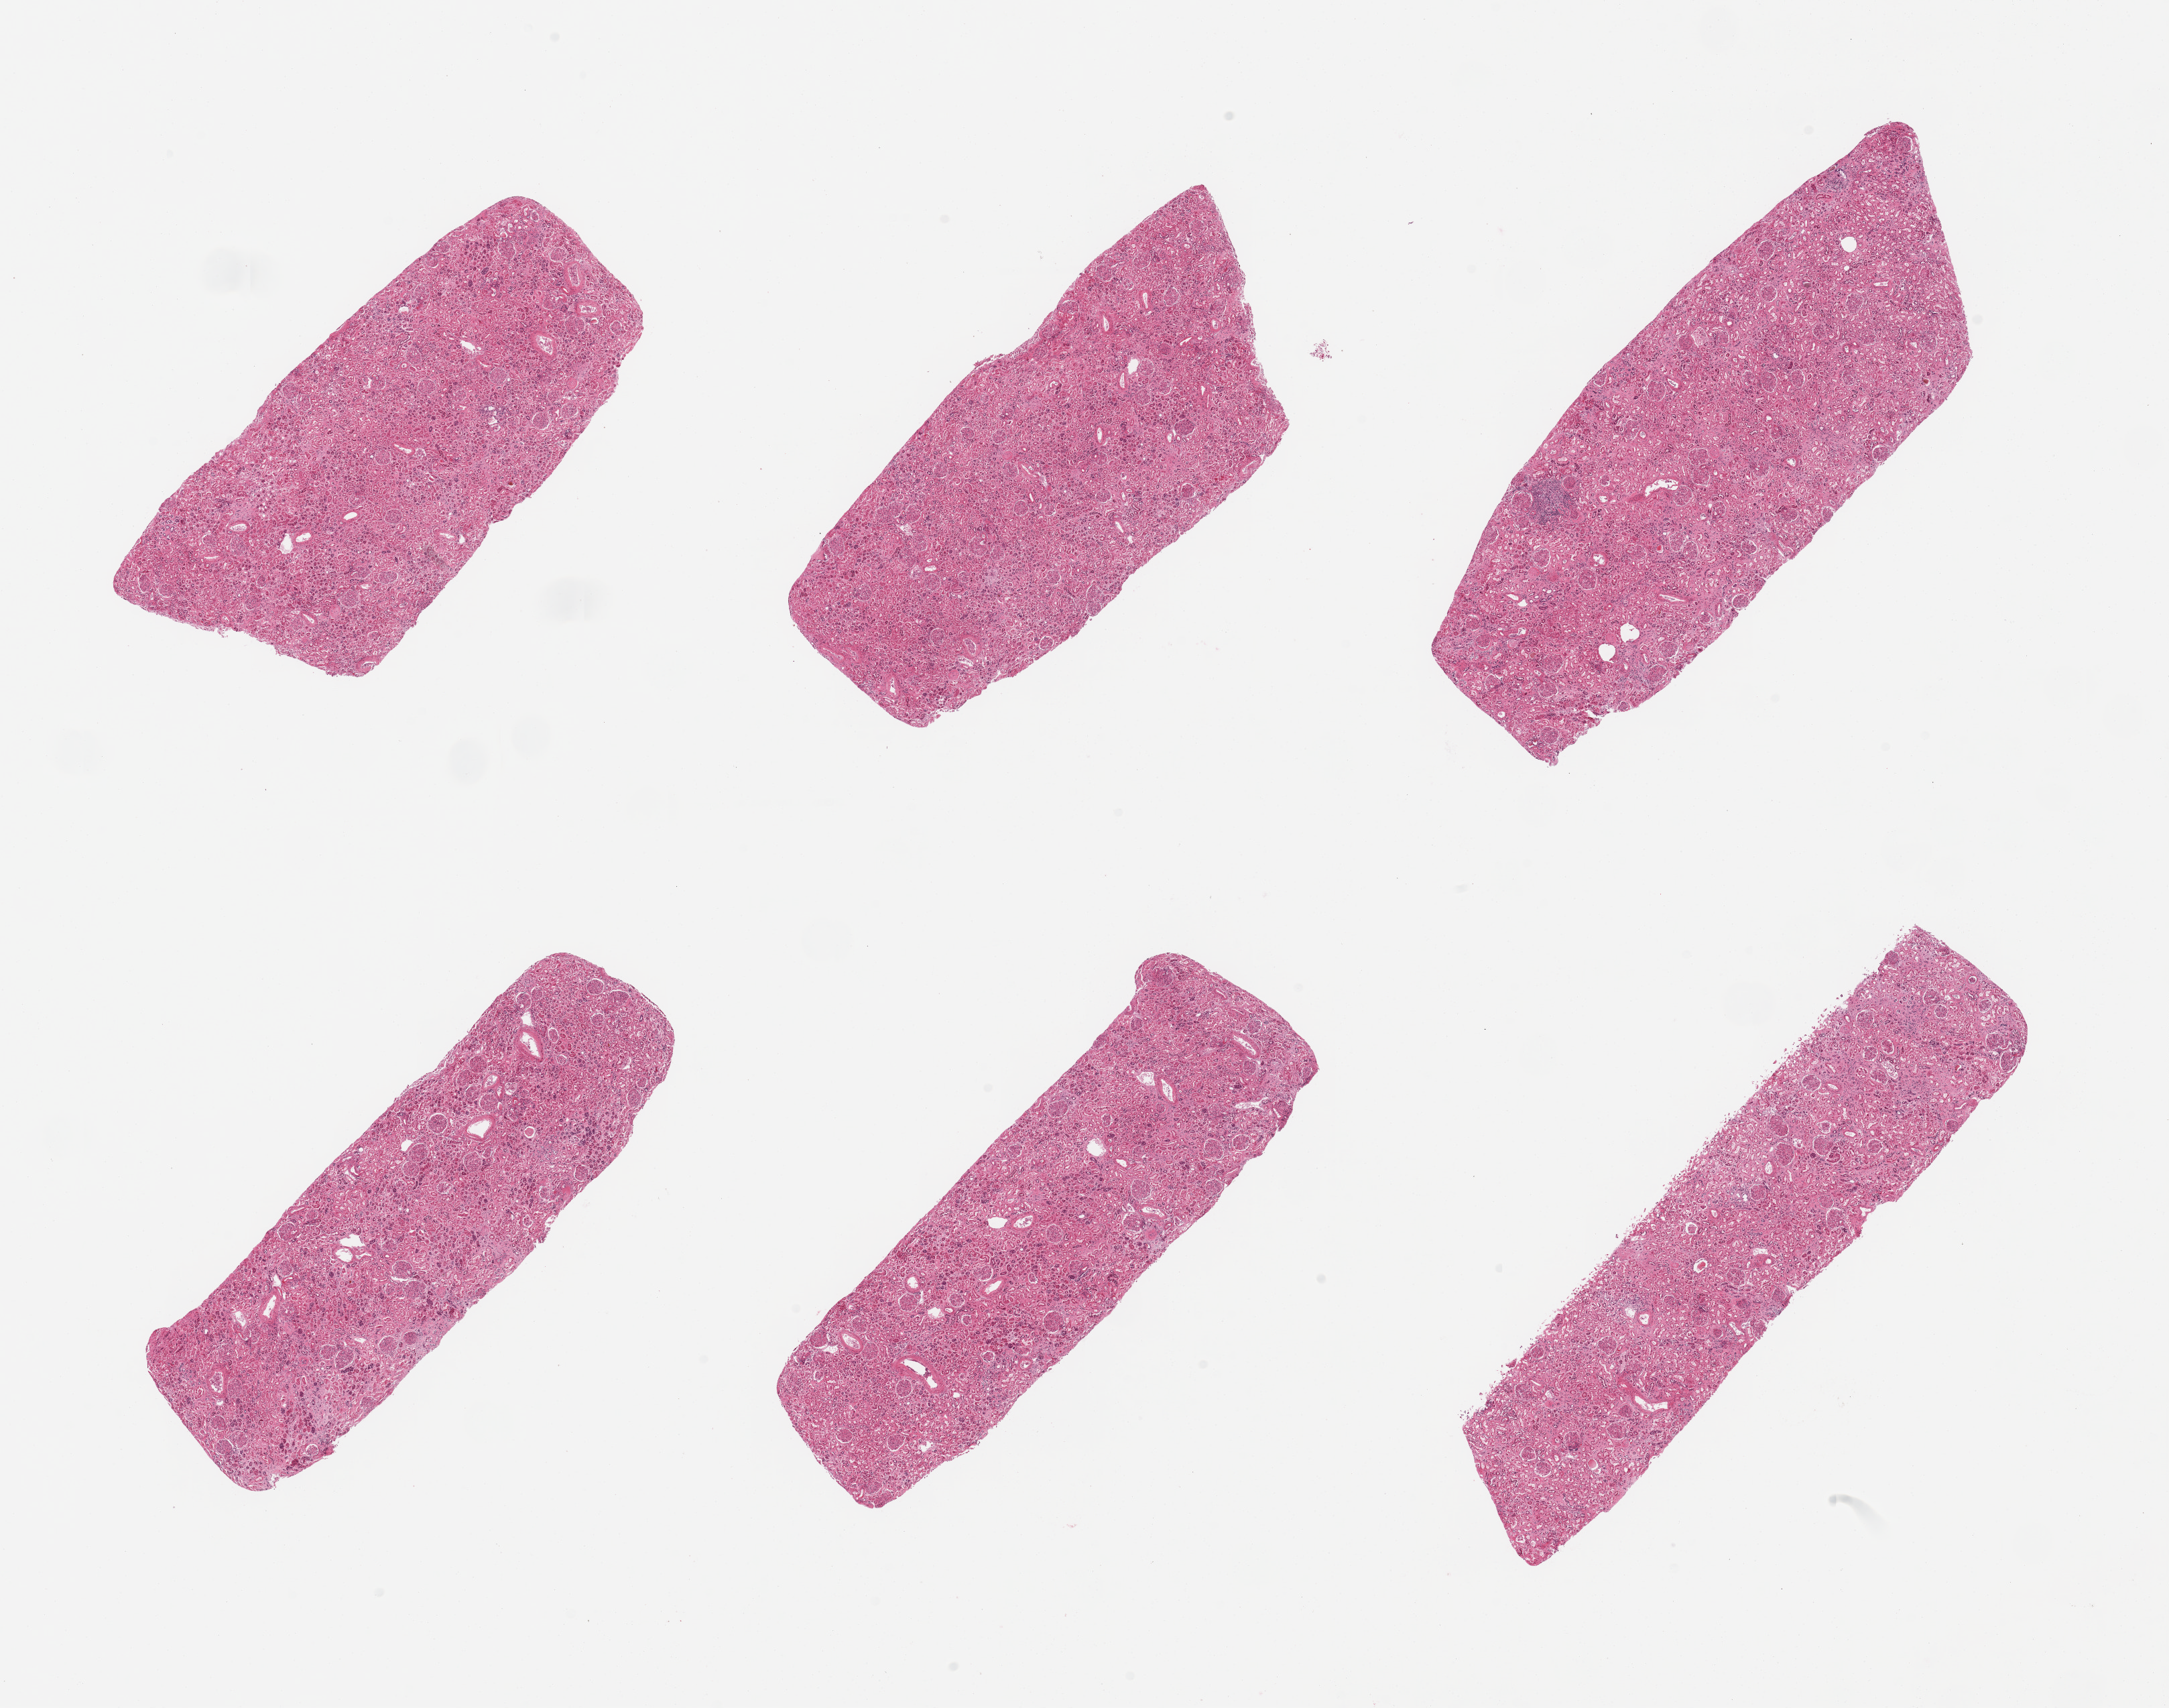
H&E whole-slide image, whole scanned area (about 25.6 x 20.2 mm) shown as a low-resolution overview, PAXgene-fixed paraffin-embedded (PFPE) section, target tissue: renal cortex, donor tissue sample. Donor: male.
Pathologist's review note for this sample: 6 pieces, glomeruli present; tubules badly preserved.